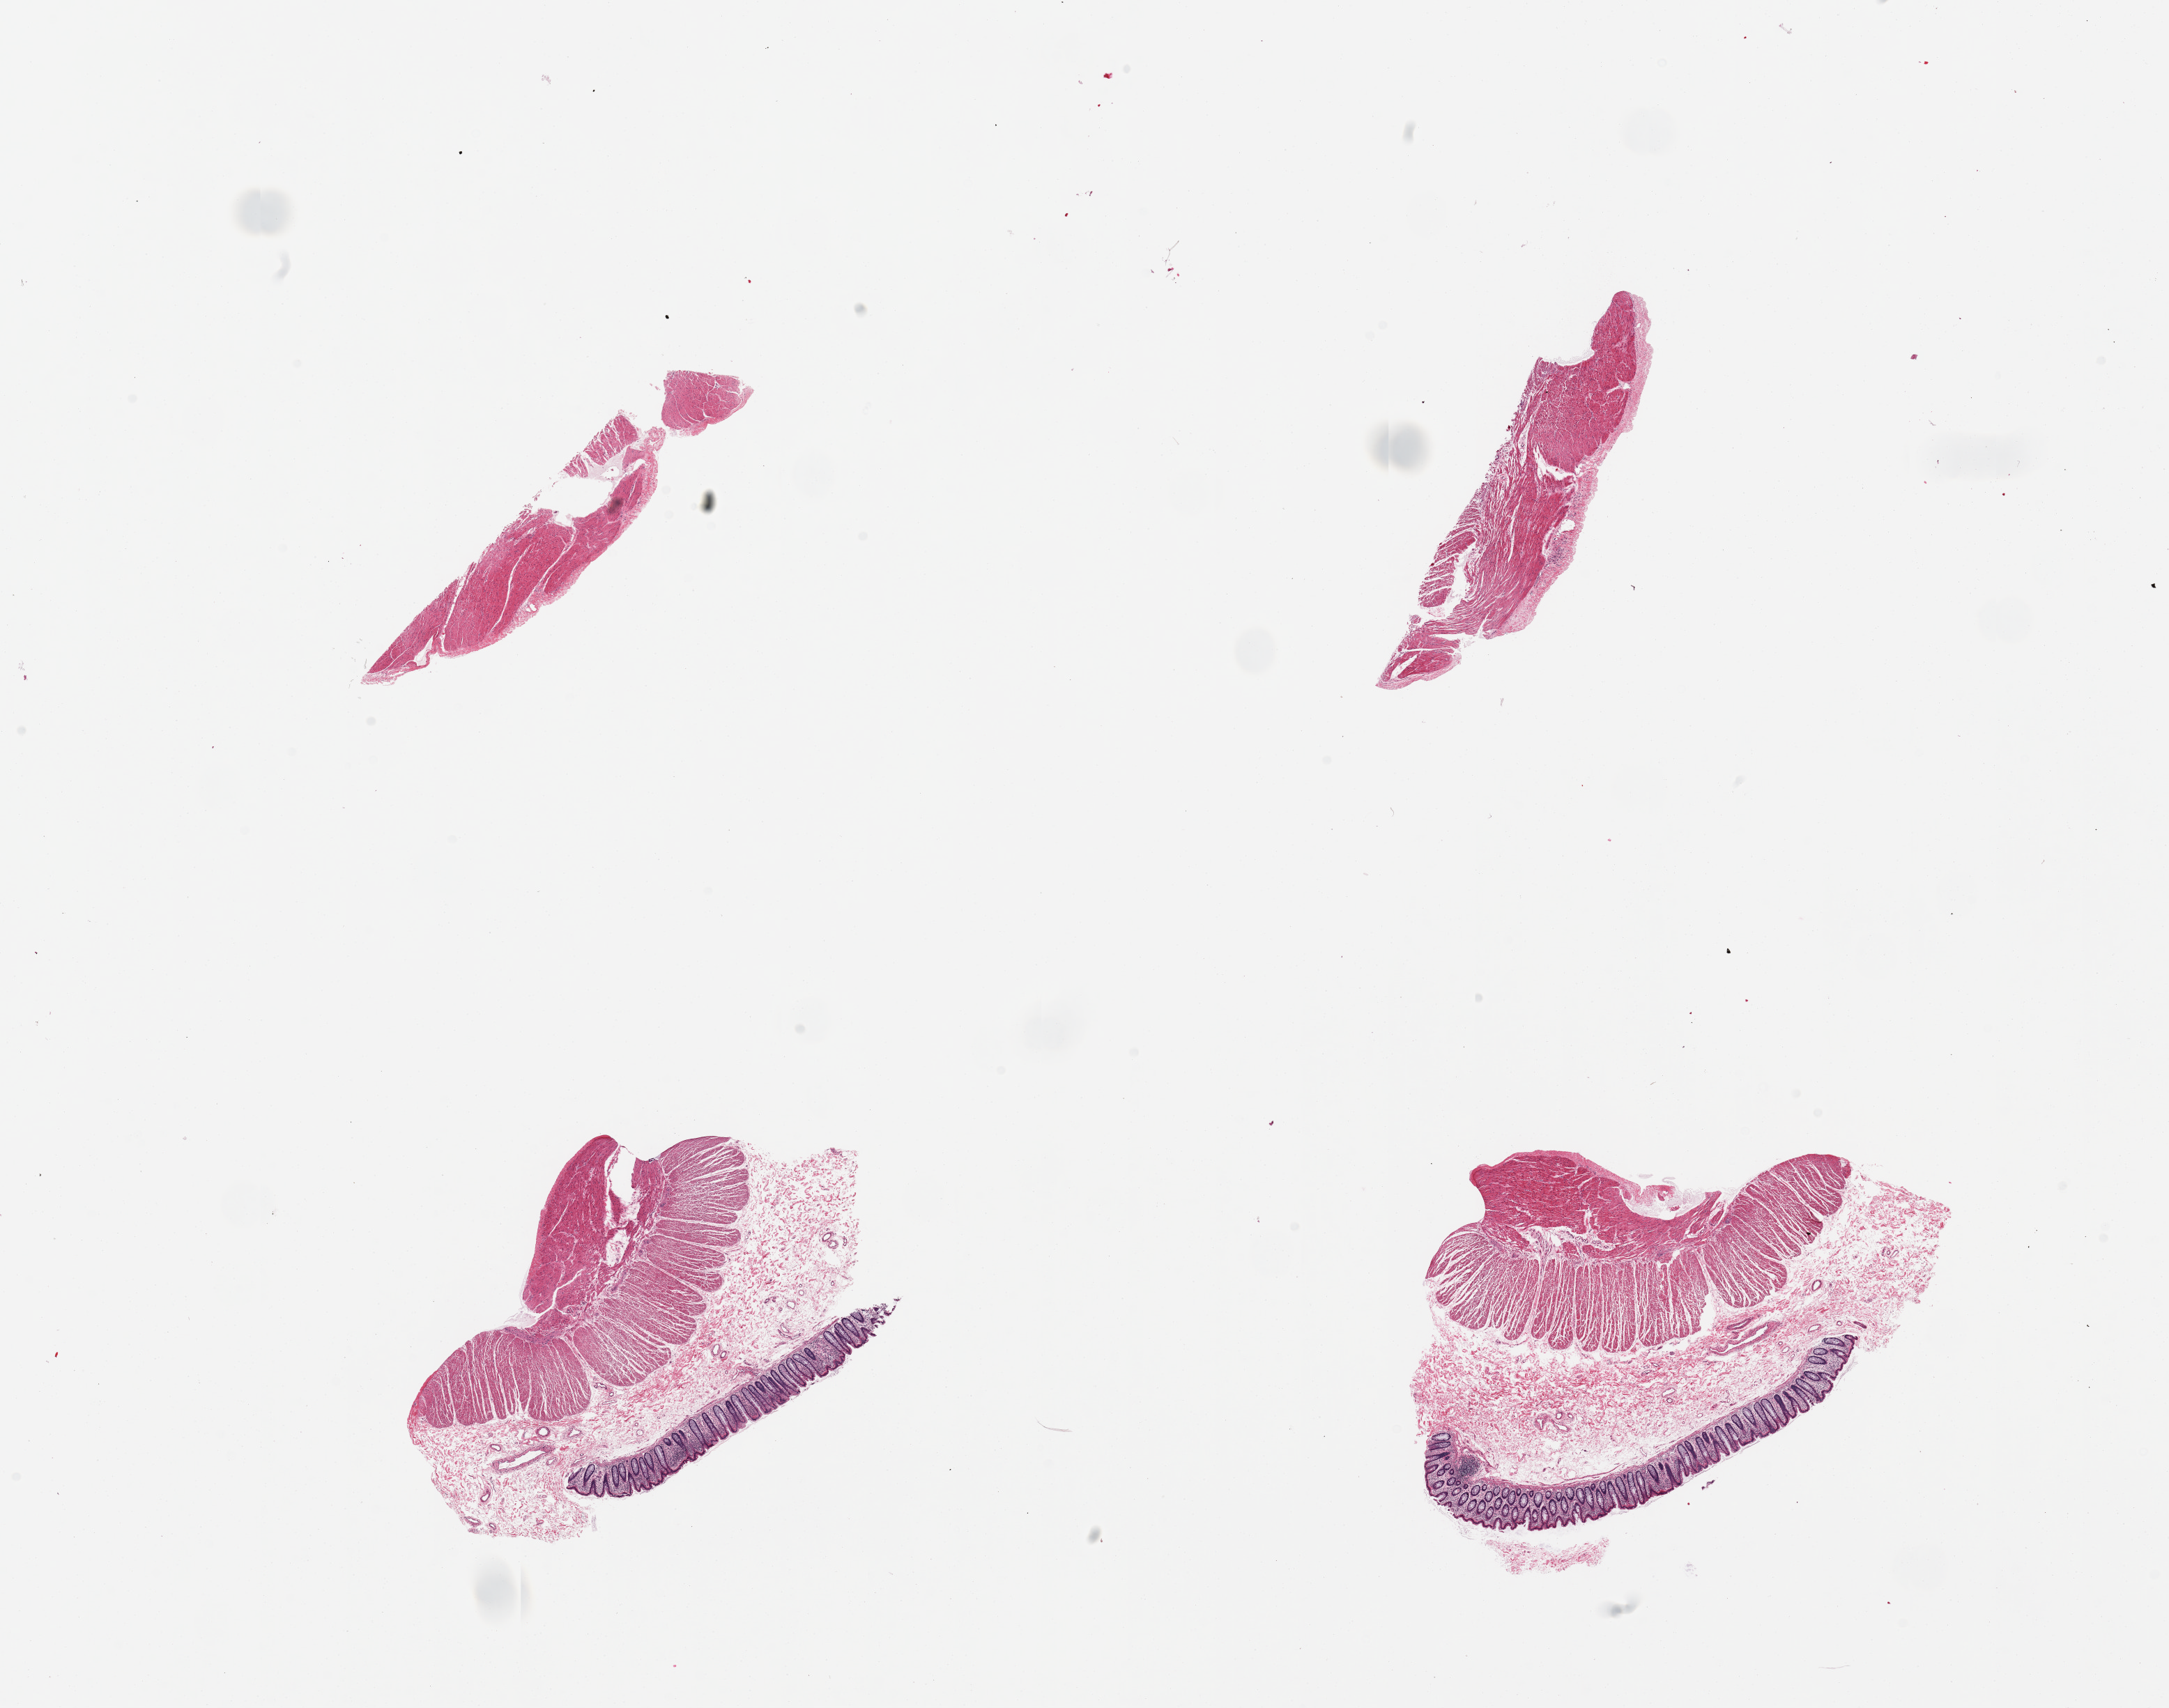
Hematoxylin and eosin (H&E) whole-slide image, low-resolution overview of the scanned area, about 24.6 x 19.4 mm (slide scanned at 20x). PAXgene-fixed paraffin-embedded (PFPE) section. Section of sigmoid colon (target tissue). Tissue donor sample. Donor: female.
Reviewer comment on this tissue sample: 4 pieces, mainly muscularis, 2 have adherent fat/mucosa, the later ~10% of specimen.